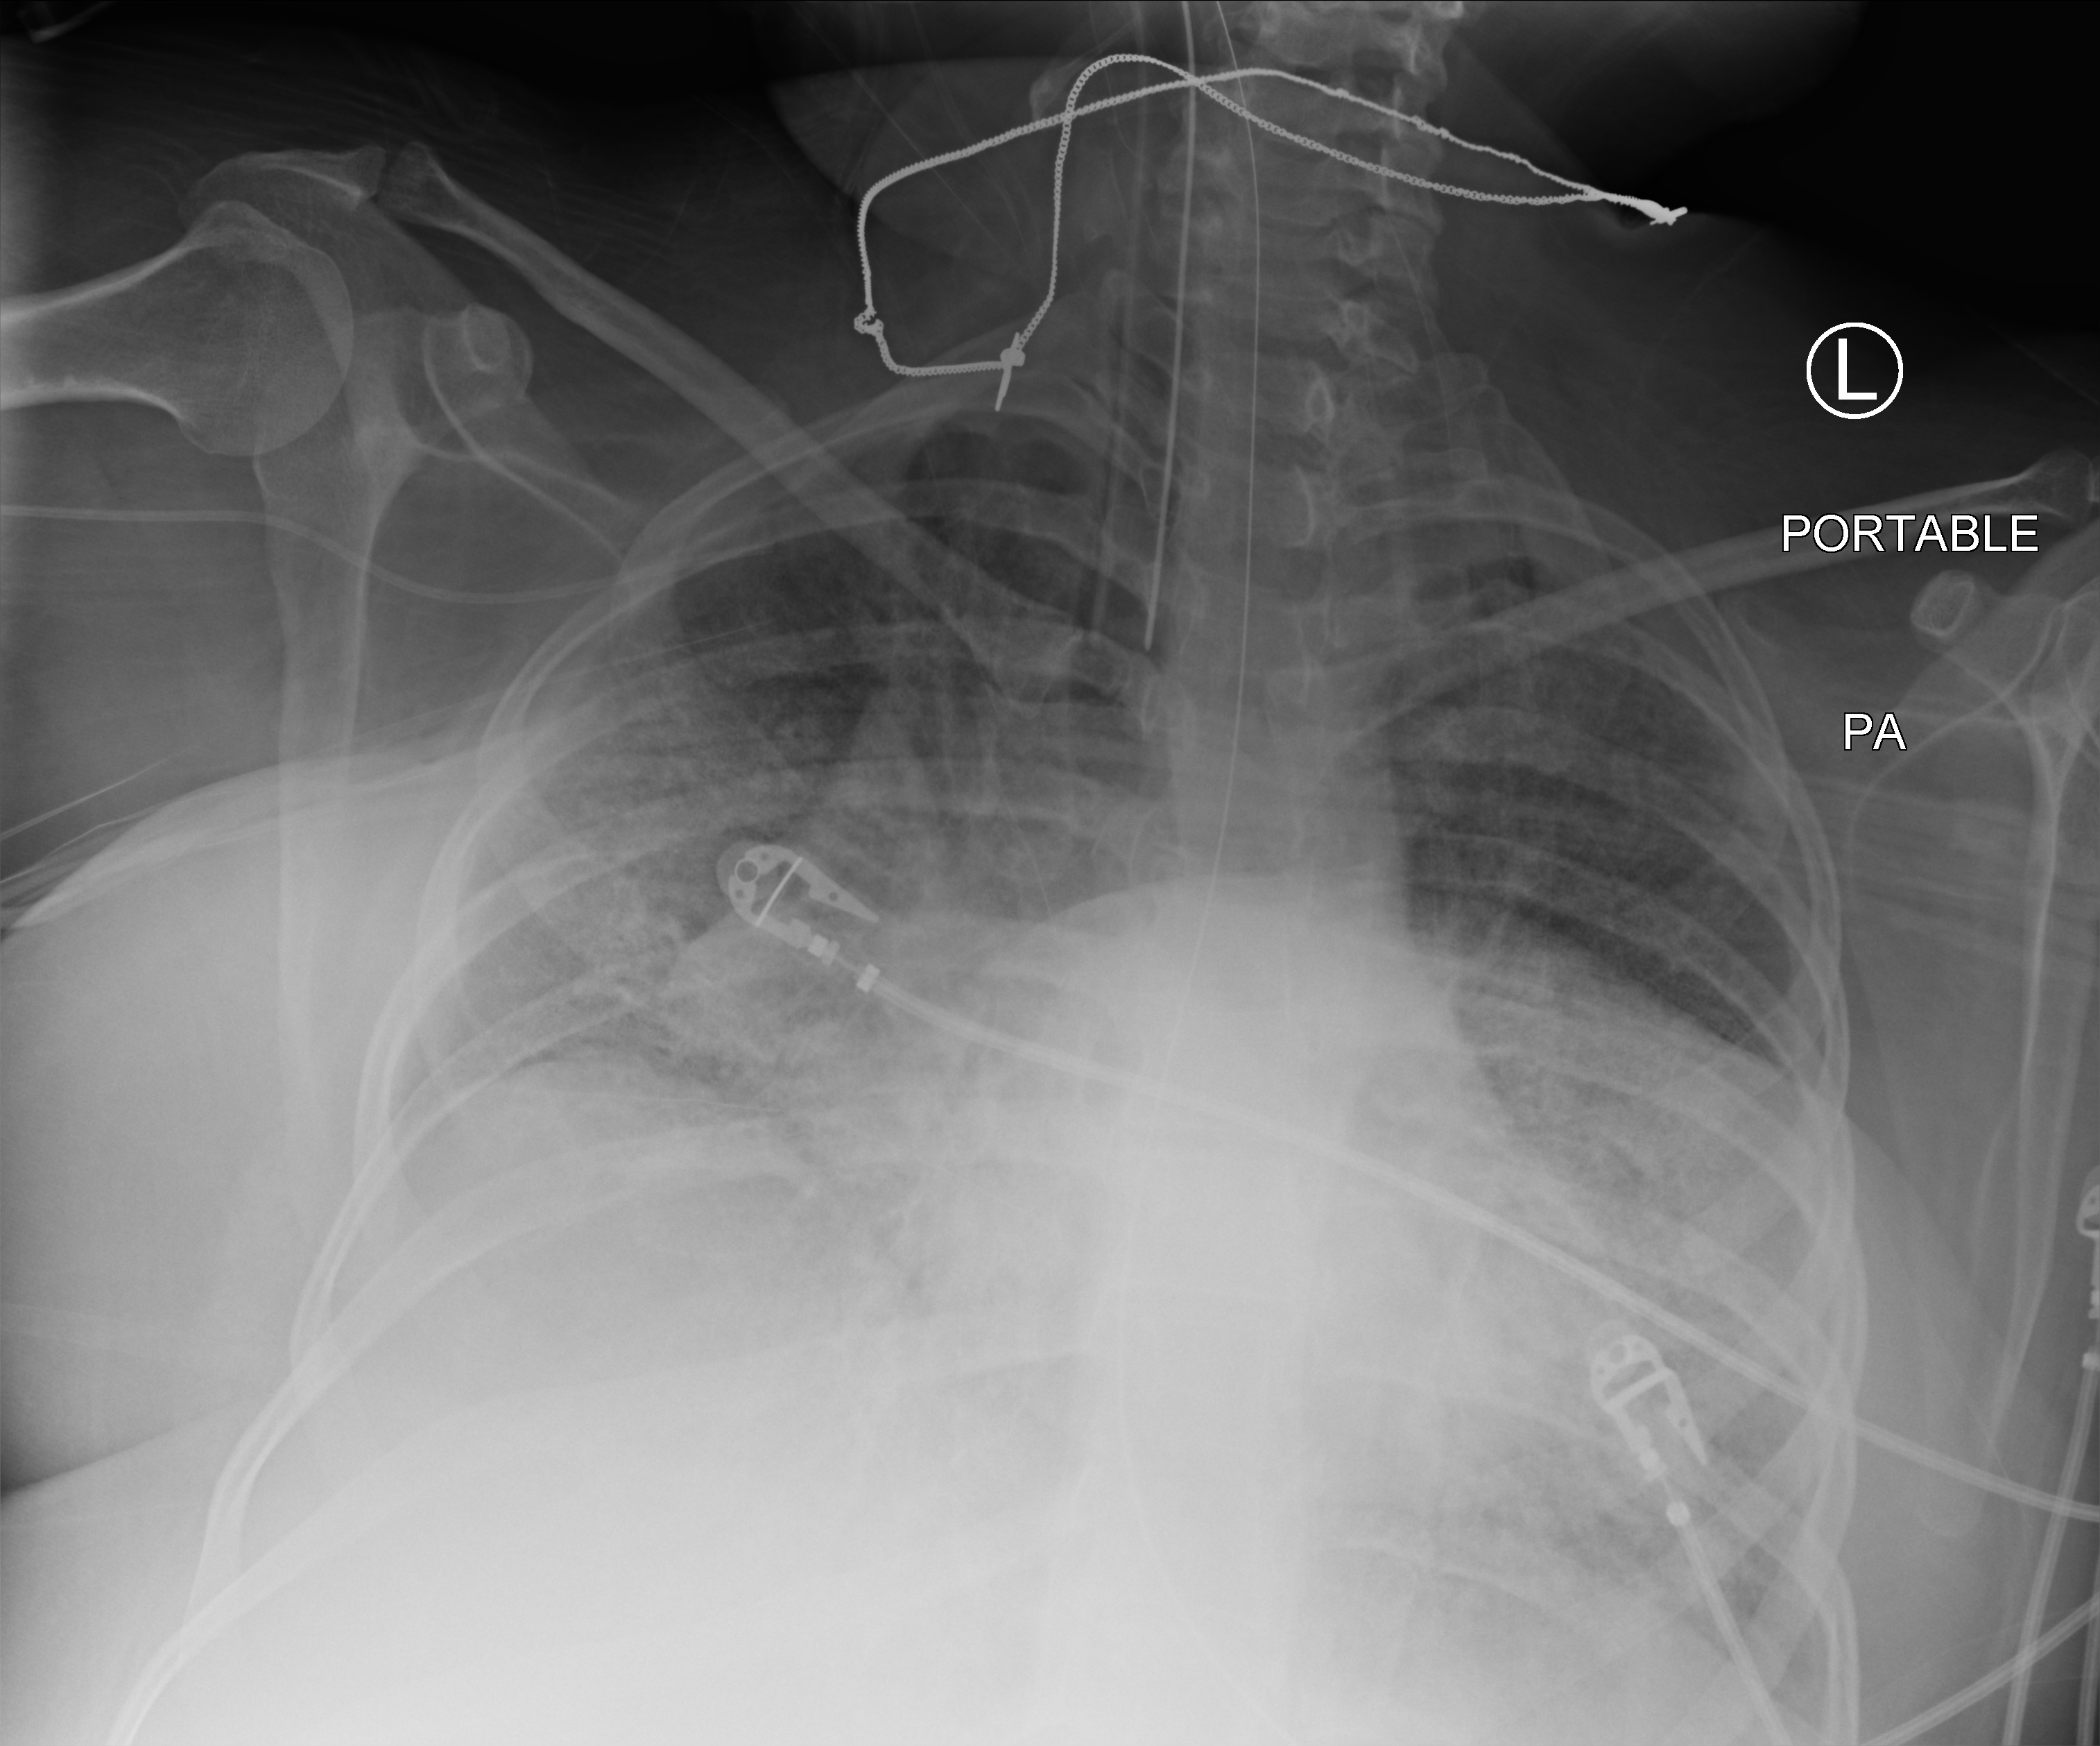
Portable chest radiograph. Patient hospitalised with COVID-19; female, aged 18–59 years.
Hospital-stay facts (about this admission, not read from this image; timing relative to this image not recorded):
- mechanically ventilated during this hospital stay: yes